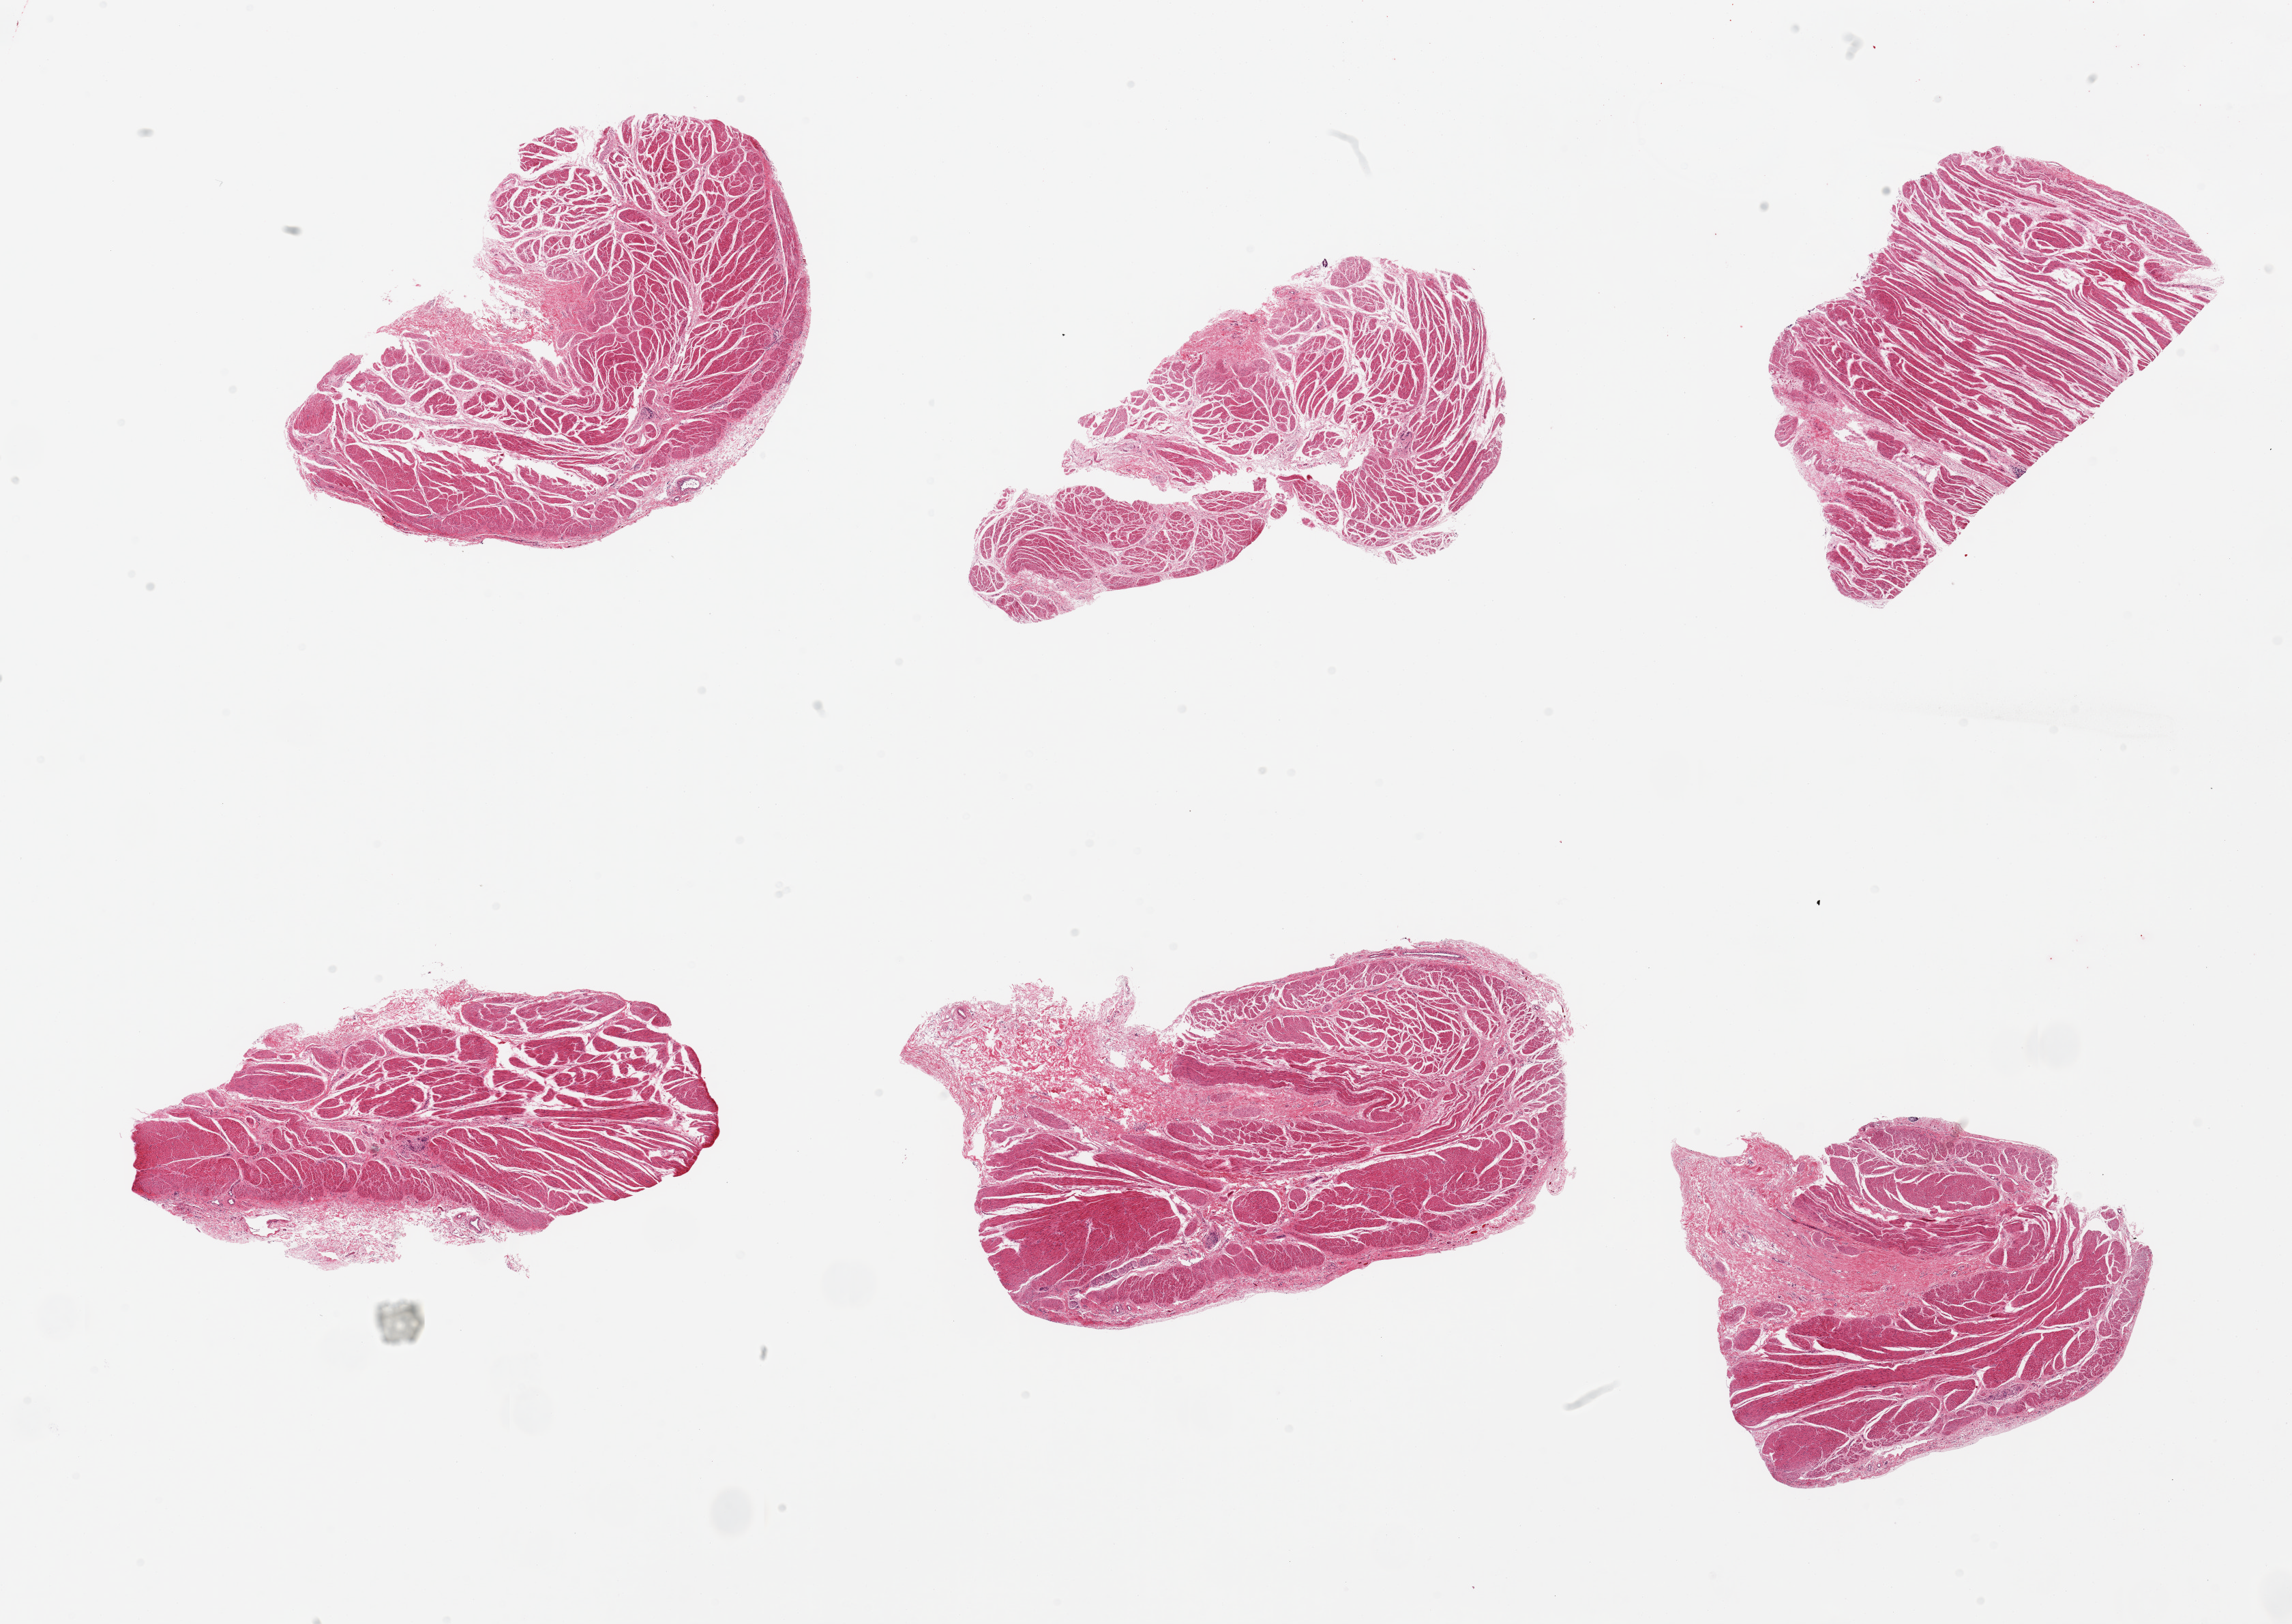
H&E whole-slide image, brightfield, whole scanned area (about 26.6 x 18.8 mm, slide scanned at 20x) shown as a low-resolution overview. Donor: male.
Specimen: PAXgene-fixed, paraffin-embedded tissue; target tissue: stomach; tissue donor sample.